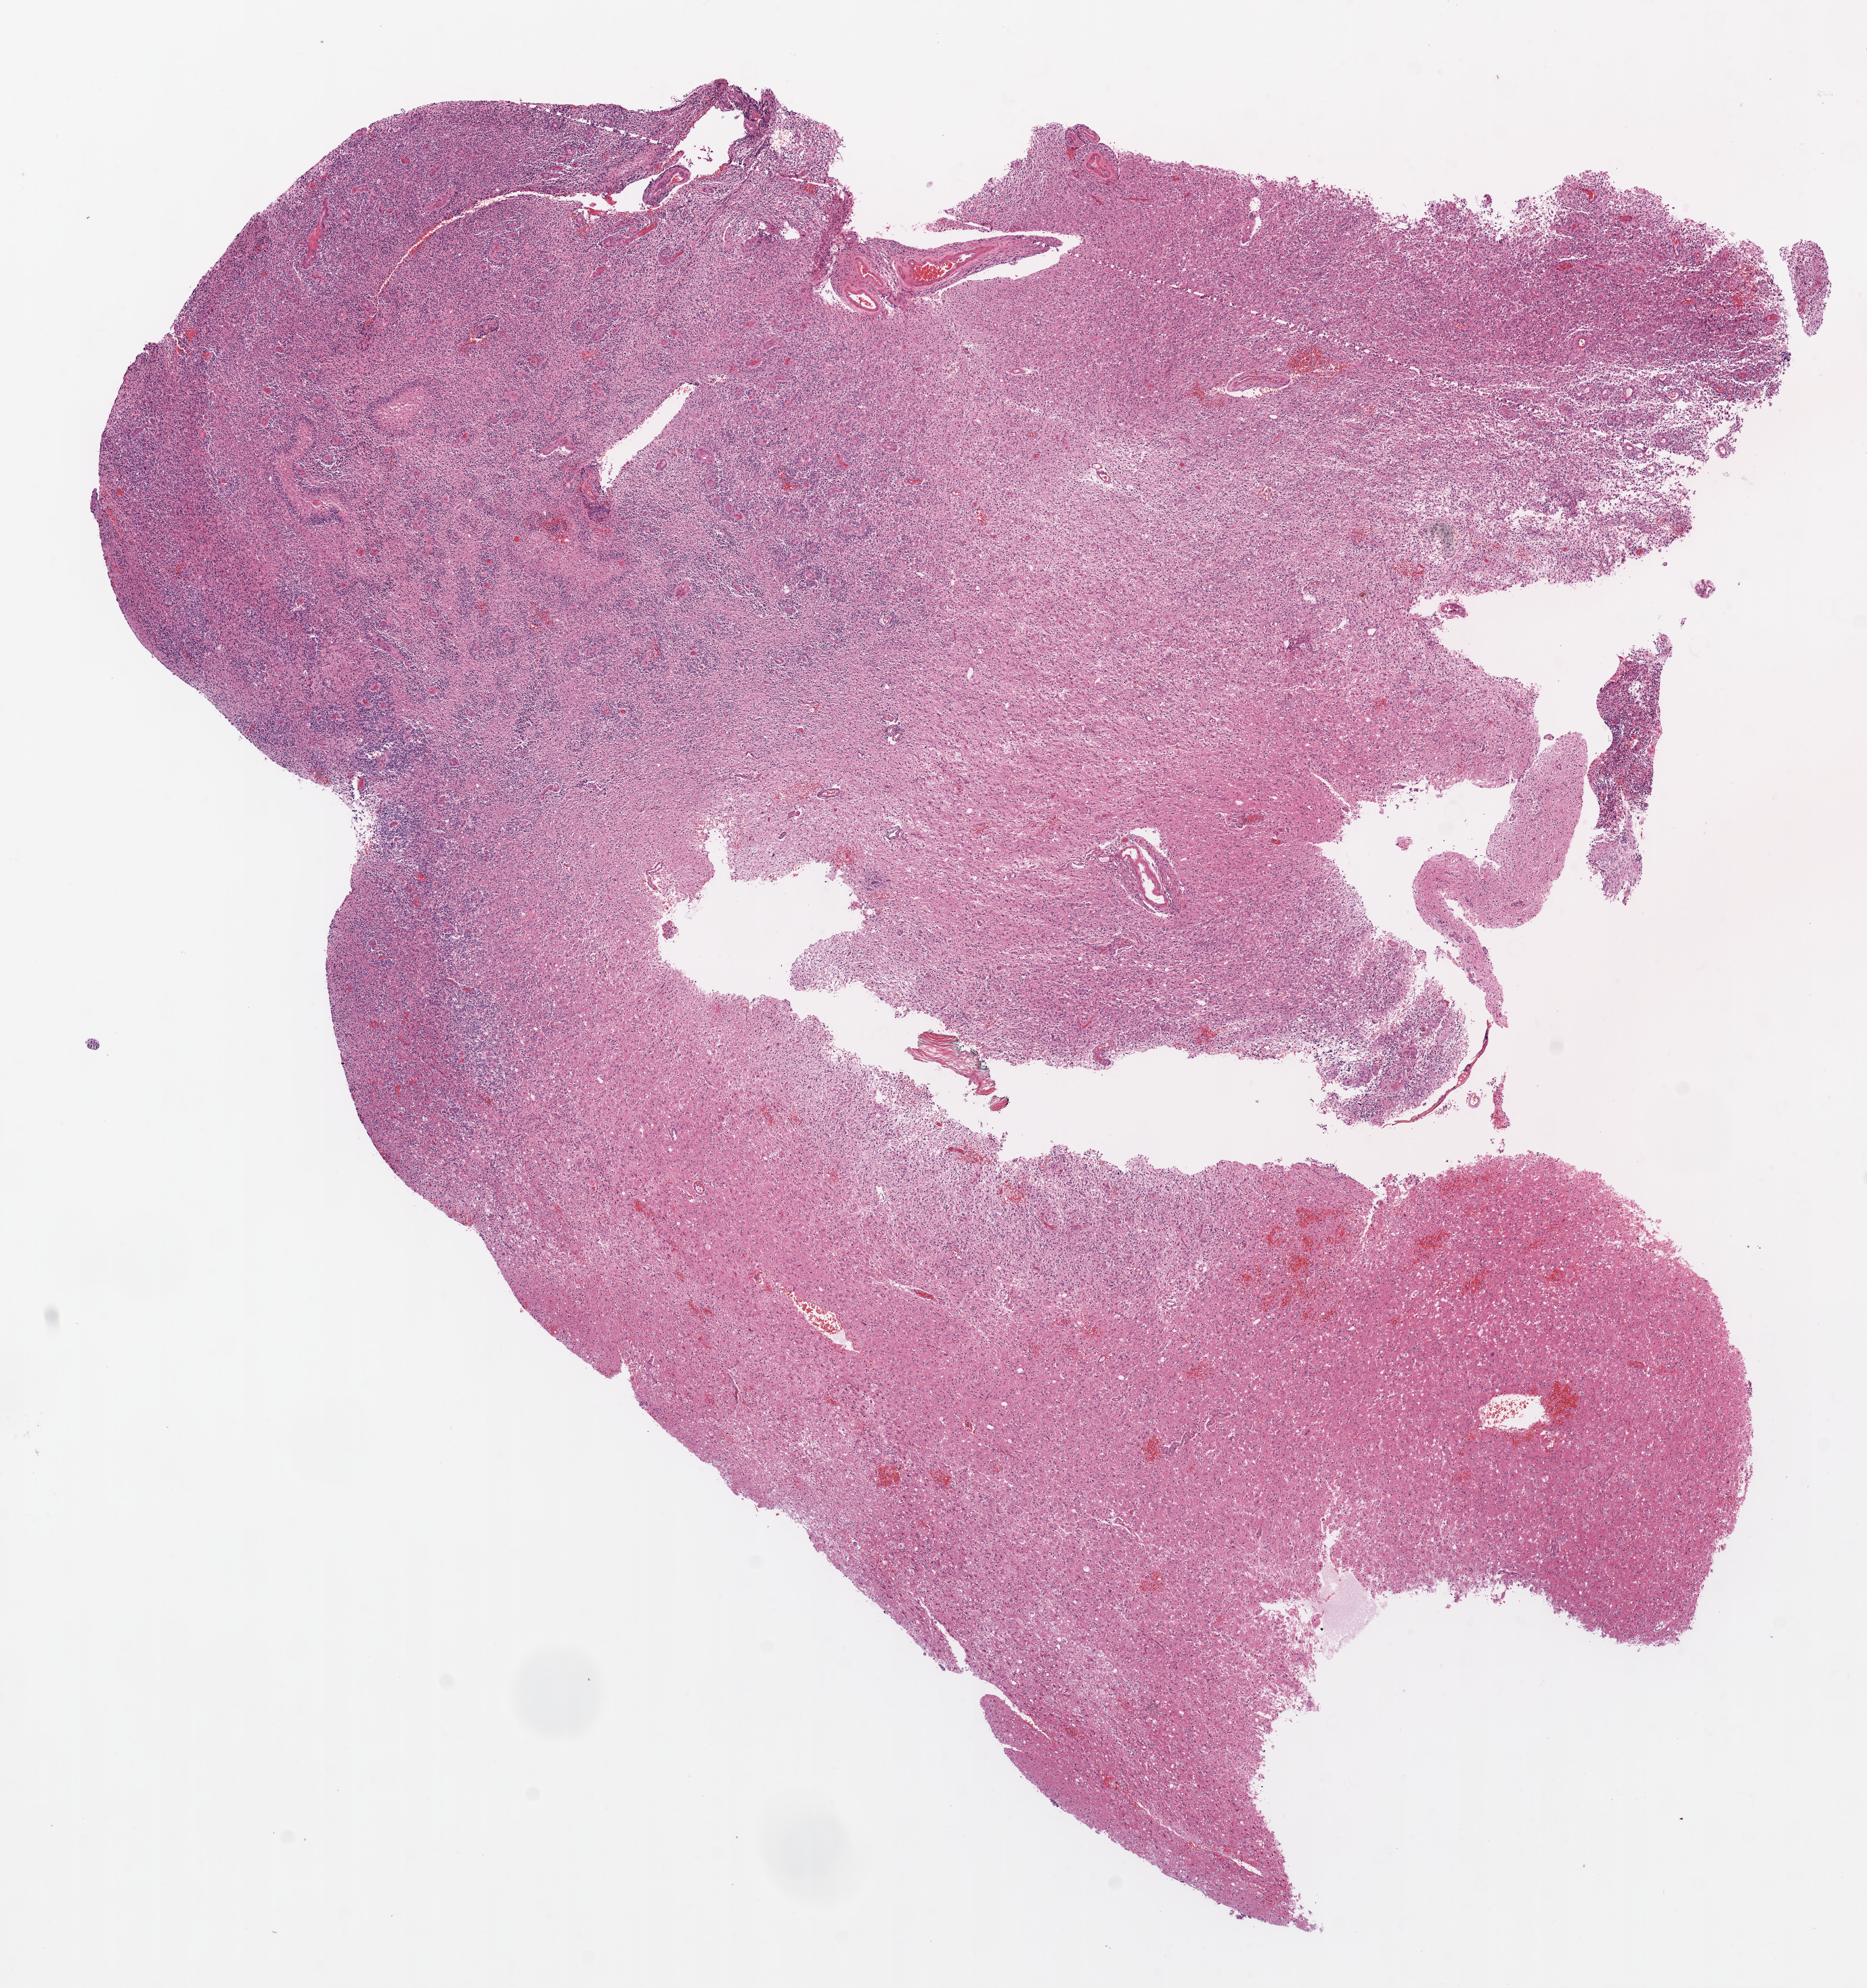
Hematoxylin and eosin (H&E) stained whole-slide image, a low-resolution overview of the entire scanned area, about 11.1 x 11.8 mm; formalin-fixed paraffin-embedded (FFPE) diagnostic section; sample: primary tumour, brain. Male patient; age at initial diagnosis 51 years.
Diagnosis: Glioblastoma.